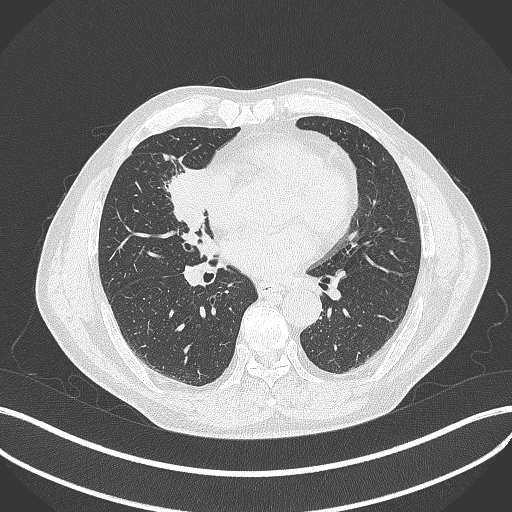
Chest CT, one axial slice; slice 185 of 429 in the series (ordered by position); lung window (W 1500 / L -600 HU); 1 mm slice thickness; 512 × 512 image matrix, field of view 400 × 400 mm. Male patient, age 61 years. Case-level facts recorded for this patient, not image findings: clinical TNM (as recorded): T2b N1 M0.
Structures marked on this image (bounding box drawn by a radiologist):
- lung tumour (recorded histology: squamous cell carcinoma): bounding box (x1, y1, x2, y2) in pixels: (158, 157, 215, 242)